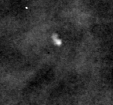
Cropped region of a digitized screen-film mammogram centred on a radiologist-marked abnormality, right breast, MLO view, BI-RADS breast density category 3 (scale 1–4).
Marked abnormality: calcifications, morphology lucent center; BI-RADS assessment category 2; subtlety rating 3 on a 1 (subtle) to 5 (obvious) scale; benign; no additional work-up was recommended (benign without callback).